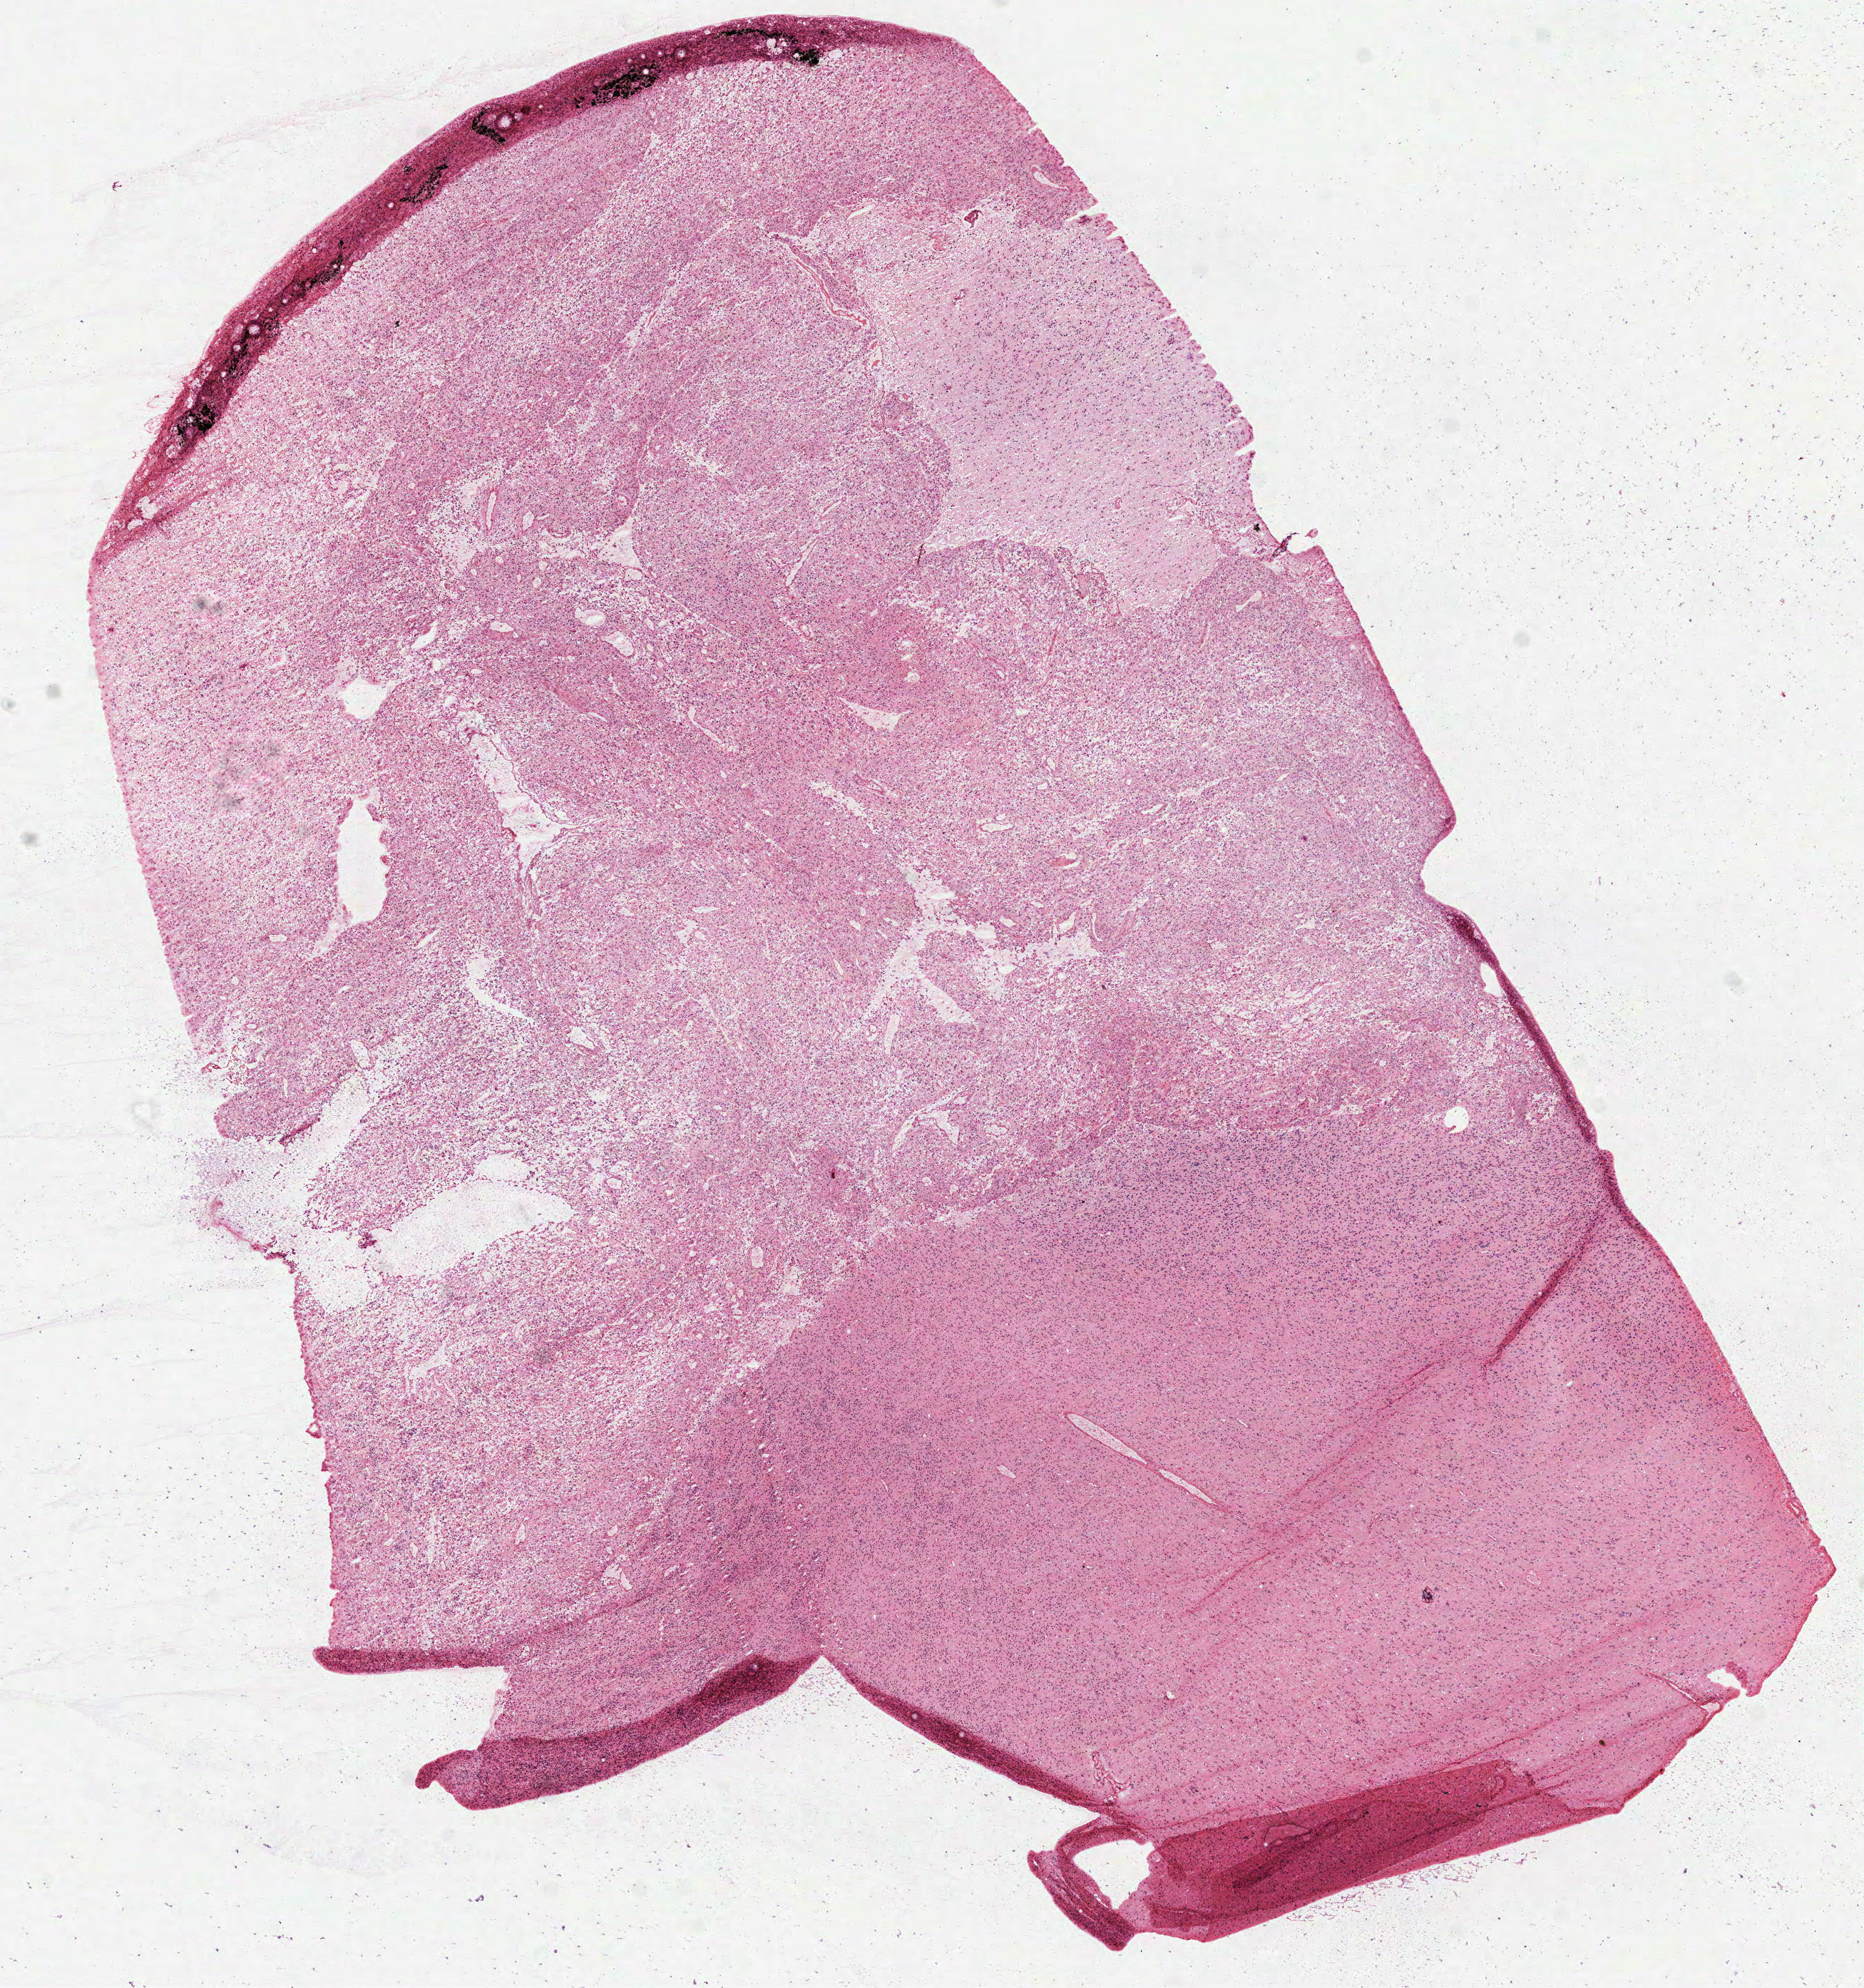
Digitized H&E tissue section (whole slide) — a low-resolution overview of the entire scanned area, about 10.5 x 11.2 mm (from a 40x scan); frozen section; brain, primary tumour sample. Female patient; age at initial diagnosis 55 years. Composition of this section per pathologist review: tumour cells 100%, tumour nuclei 80%, normal cells 0%, stromal cells 0%, necrosis 0%.
Pathologic diagnosis: Glioblastoma.